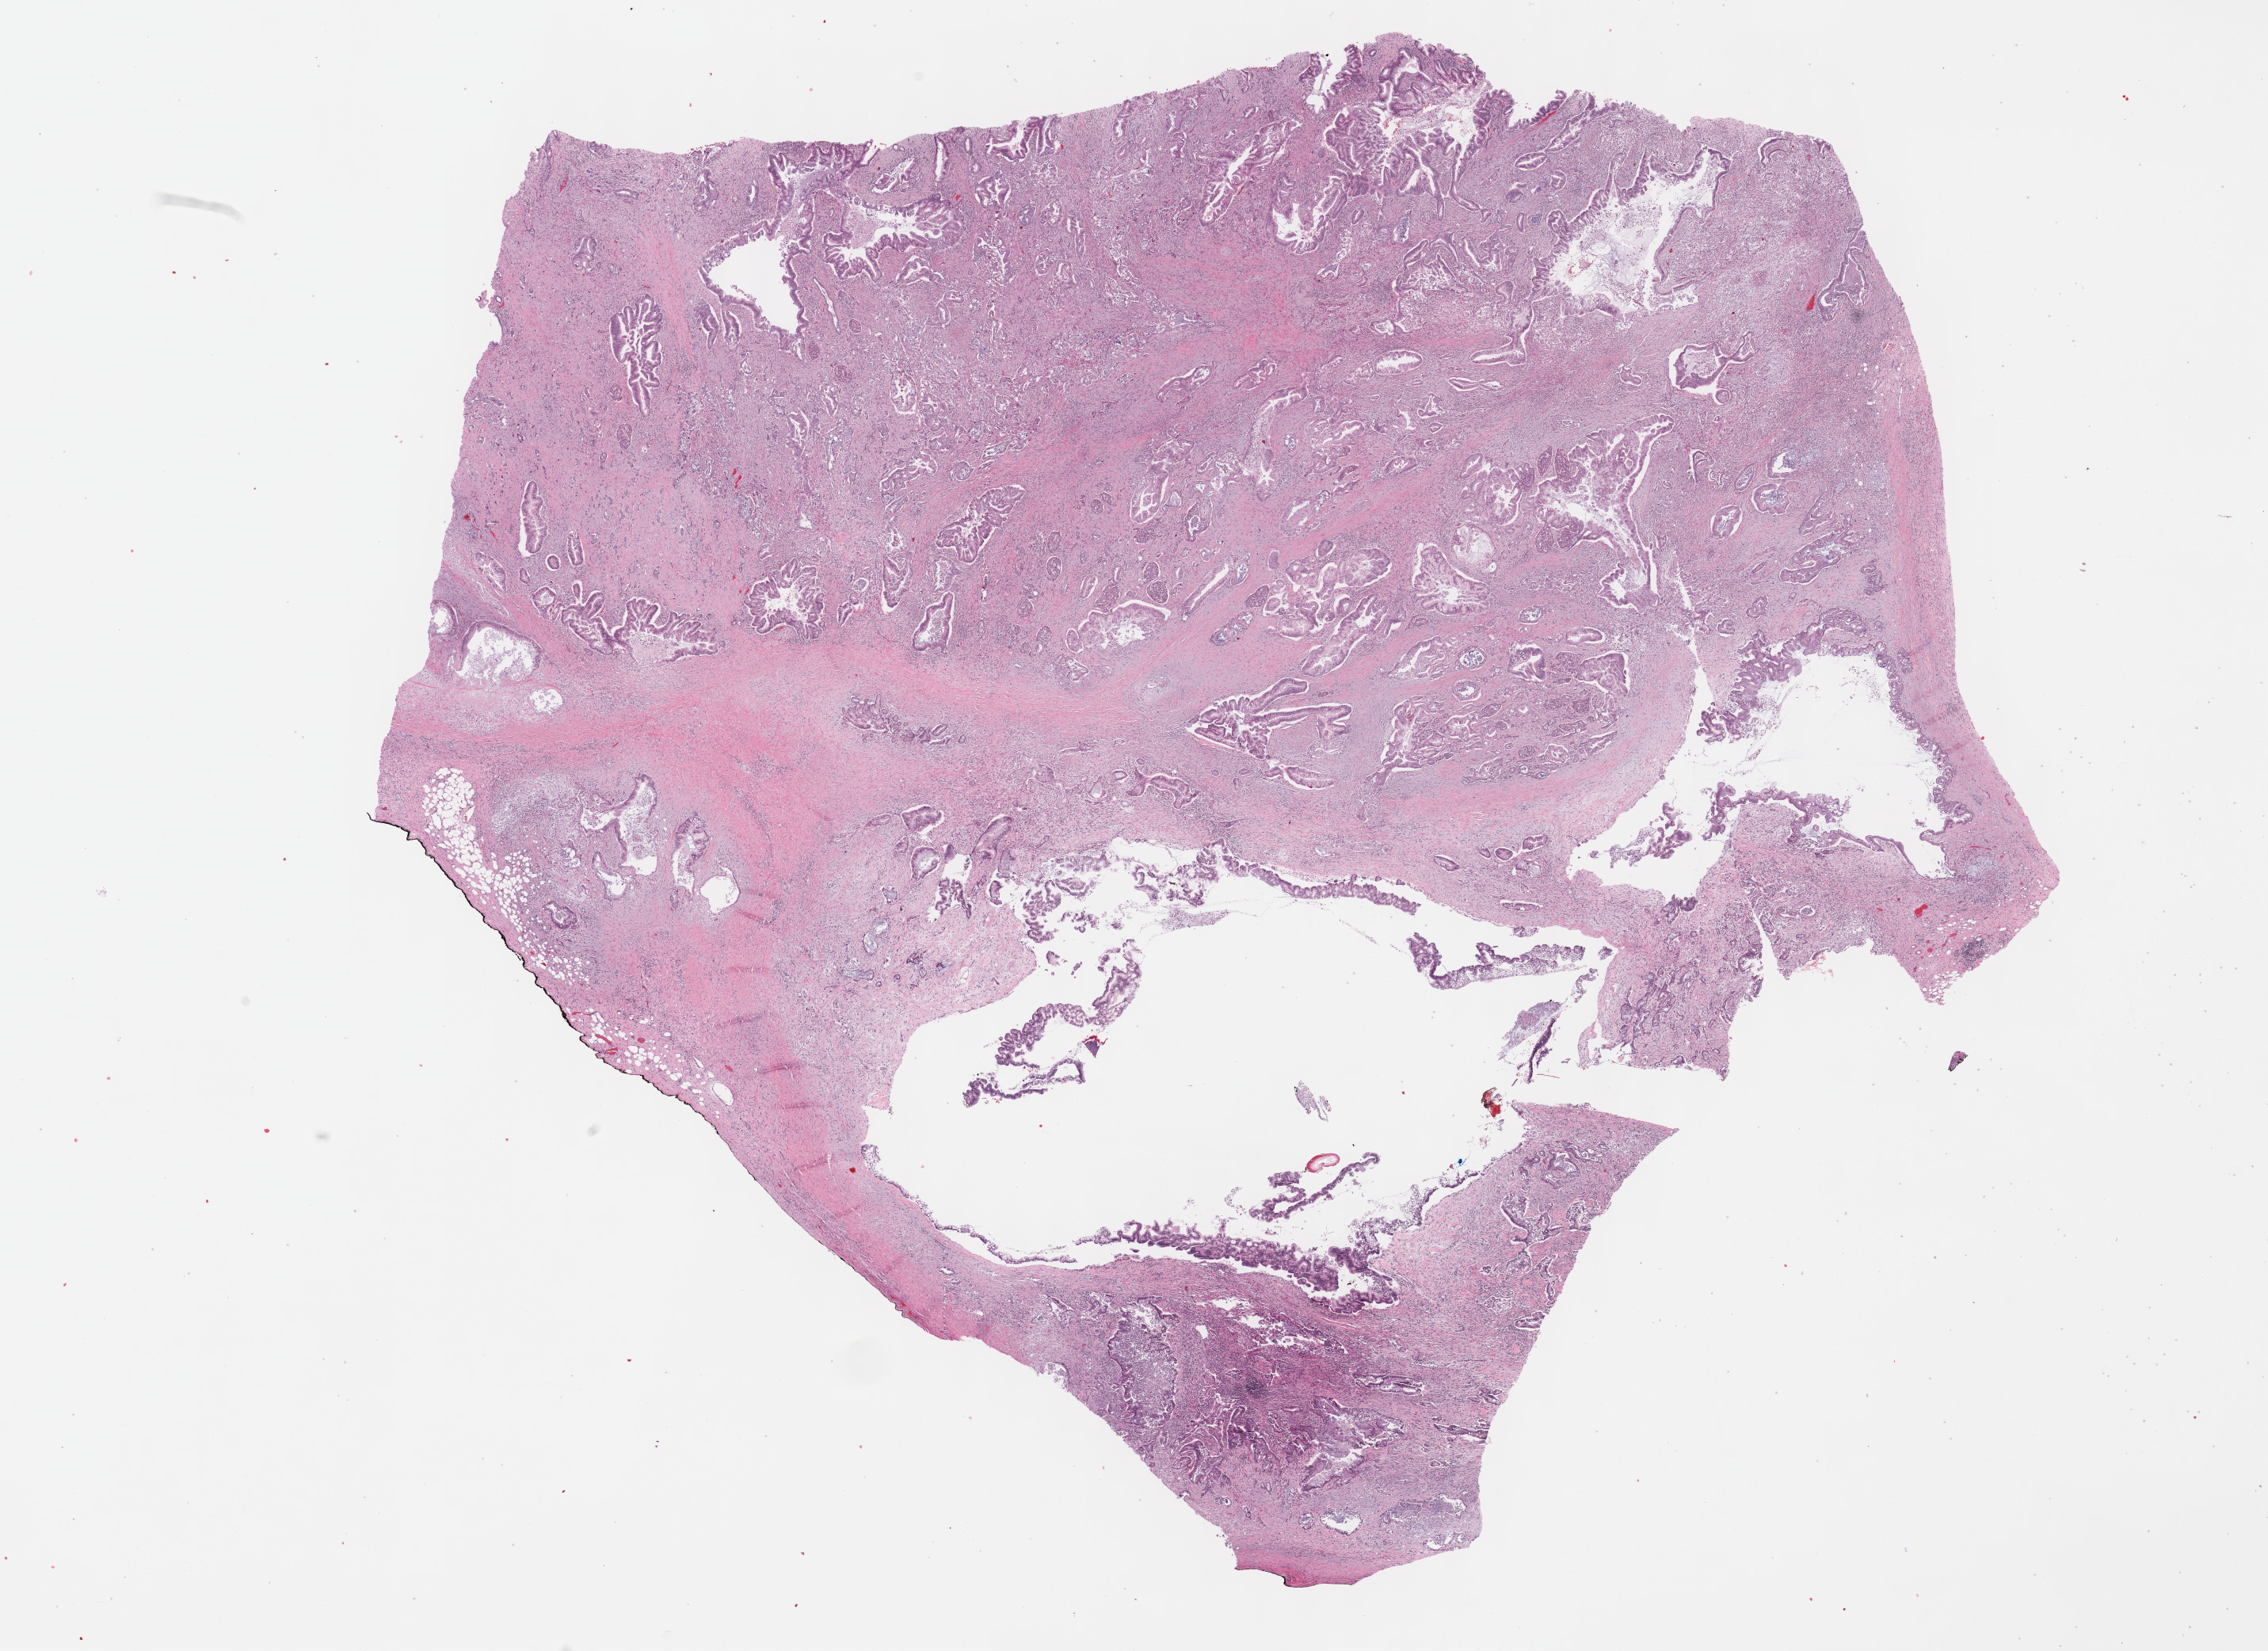
H&E-stained whole-slide image, a low-resolution overview of the entire scanned area, about 23.2 x 16.9 mm; FFPE section; primary tumour sample from the pancreas. Patient: male, age at initial diagnosis 75 years. Histologic grade: G1 (well differentiated).
AJCC pathologic stage: IIA (7th edition). Lymph nodes positive (case pathology): 0 of 22 examined. Histologic diagnosis: Infiltrating duct carcinoma, NOS (tail of pancreas).